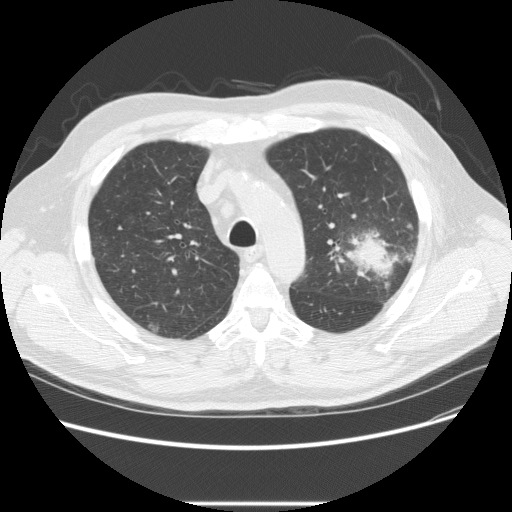
Axial slice from a low-dose chest CT screening exam, first (baseline) screen, lung window (W 1500 / L -600 HU), 2.5 mm slice thickness, 120 kVp, slice 66 of 233 in the series. Male participant, aged 73 years at enrolment. Former smoker at enrolment.
Expert reader's lesion annotation, bounding box [x1, y1, x2, y2] px = [332, 215, 418, 287]. The screening reader recorded 2 non-calcified nodules or masses ≥4 mm on this exam (left upper lobe, right upper lobe); which of them this box marks is not recorded. Lung cancer was diagnosed 11 days after this screen: bronchiolo-alveolar adenocarcinoma, NOS, other location, well differentiated (G1), stage IV (AJCC 6th edition).